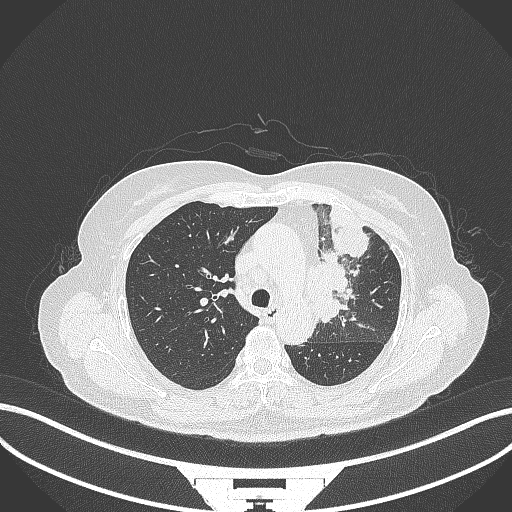
Chest CT, one axial slice. Position 232 of 382 along the scan axis. Reconstruction kernel B70f. 120 kVp. Lung window (W 1500 / L -600 HU). 1 mm slice thickness. 512 × 512 image matrix, field of view 400 × 400 mm. Female patient, age 64 years. Case-level facts recorded for this patient, not image findings: clinical TNM (as recorded): T2a N2 M0.
Structures marked on this image (rectangle marked by the reading radiologist):
- lung tumour (recorded histology: adenocarcinoma): bounding box [x1, y1, x2, y2] px = [301, 249, 353, 324]
- lung tumour (recorded histology: adenocarcinoma): [330, 221, 373, 262]